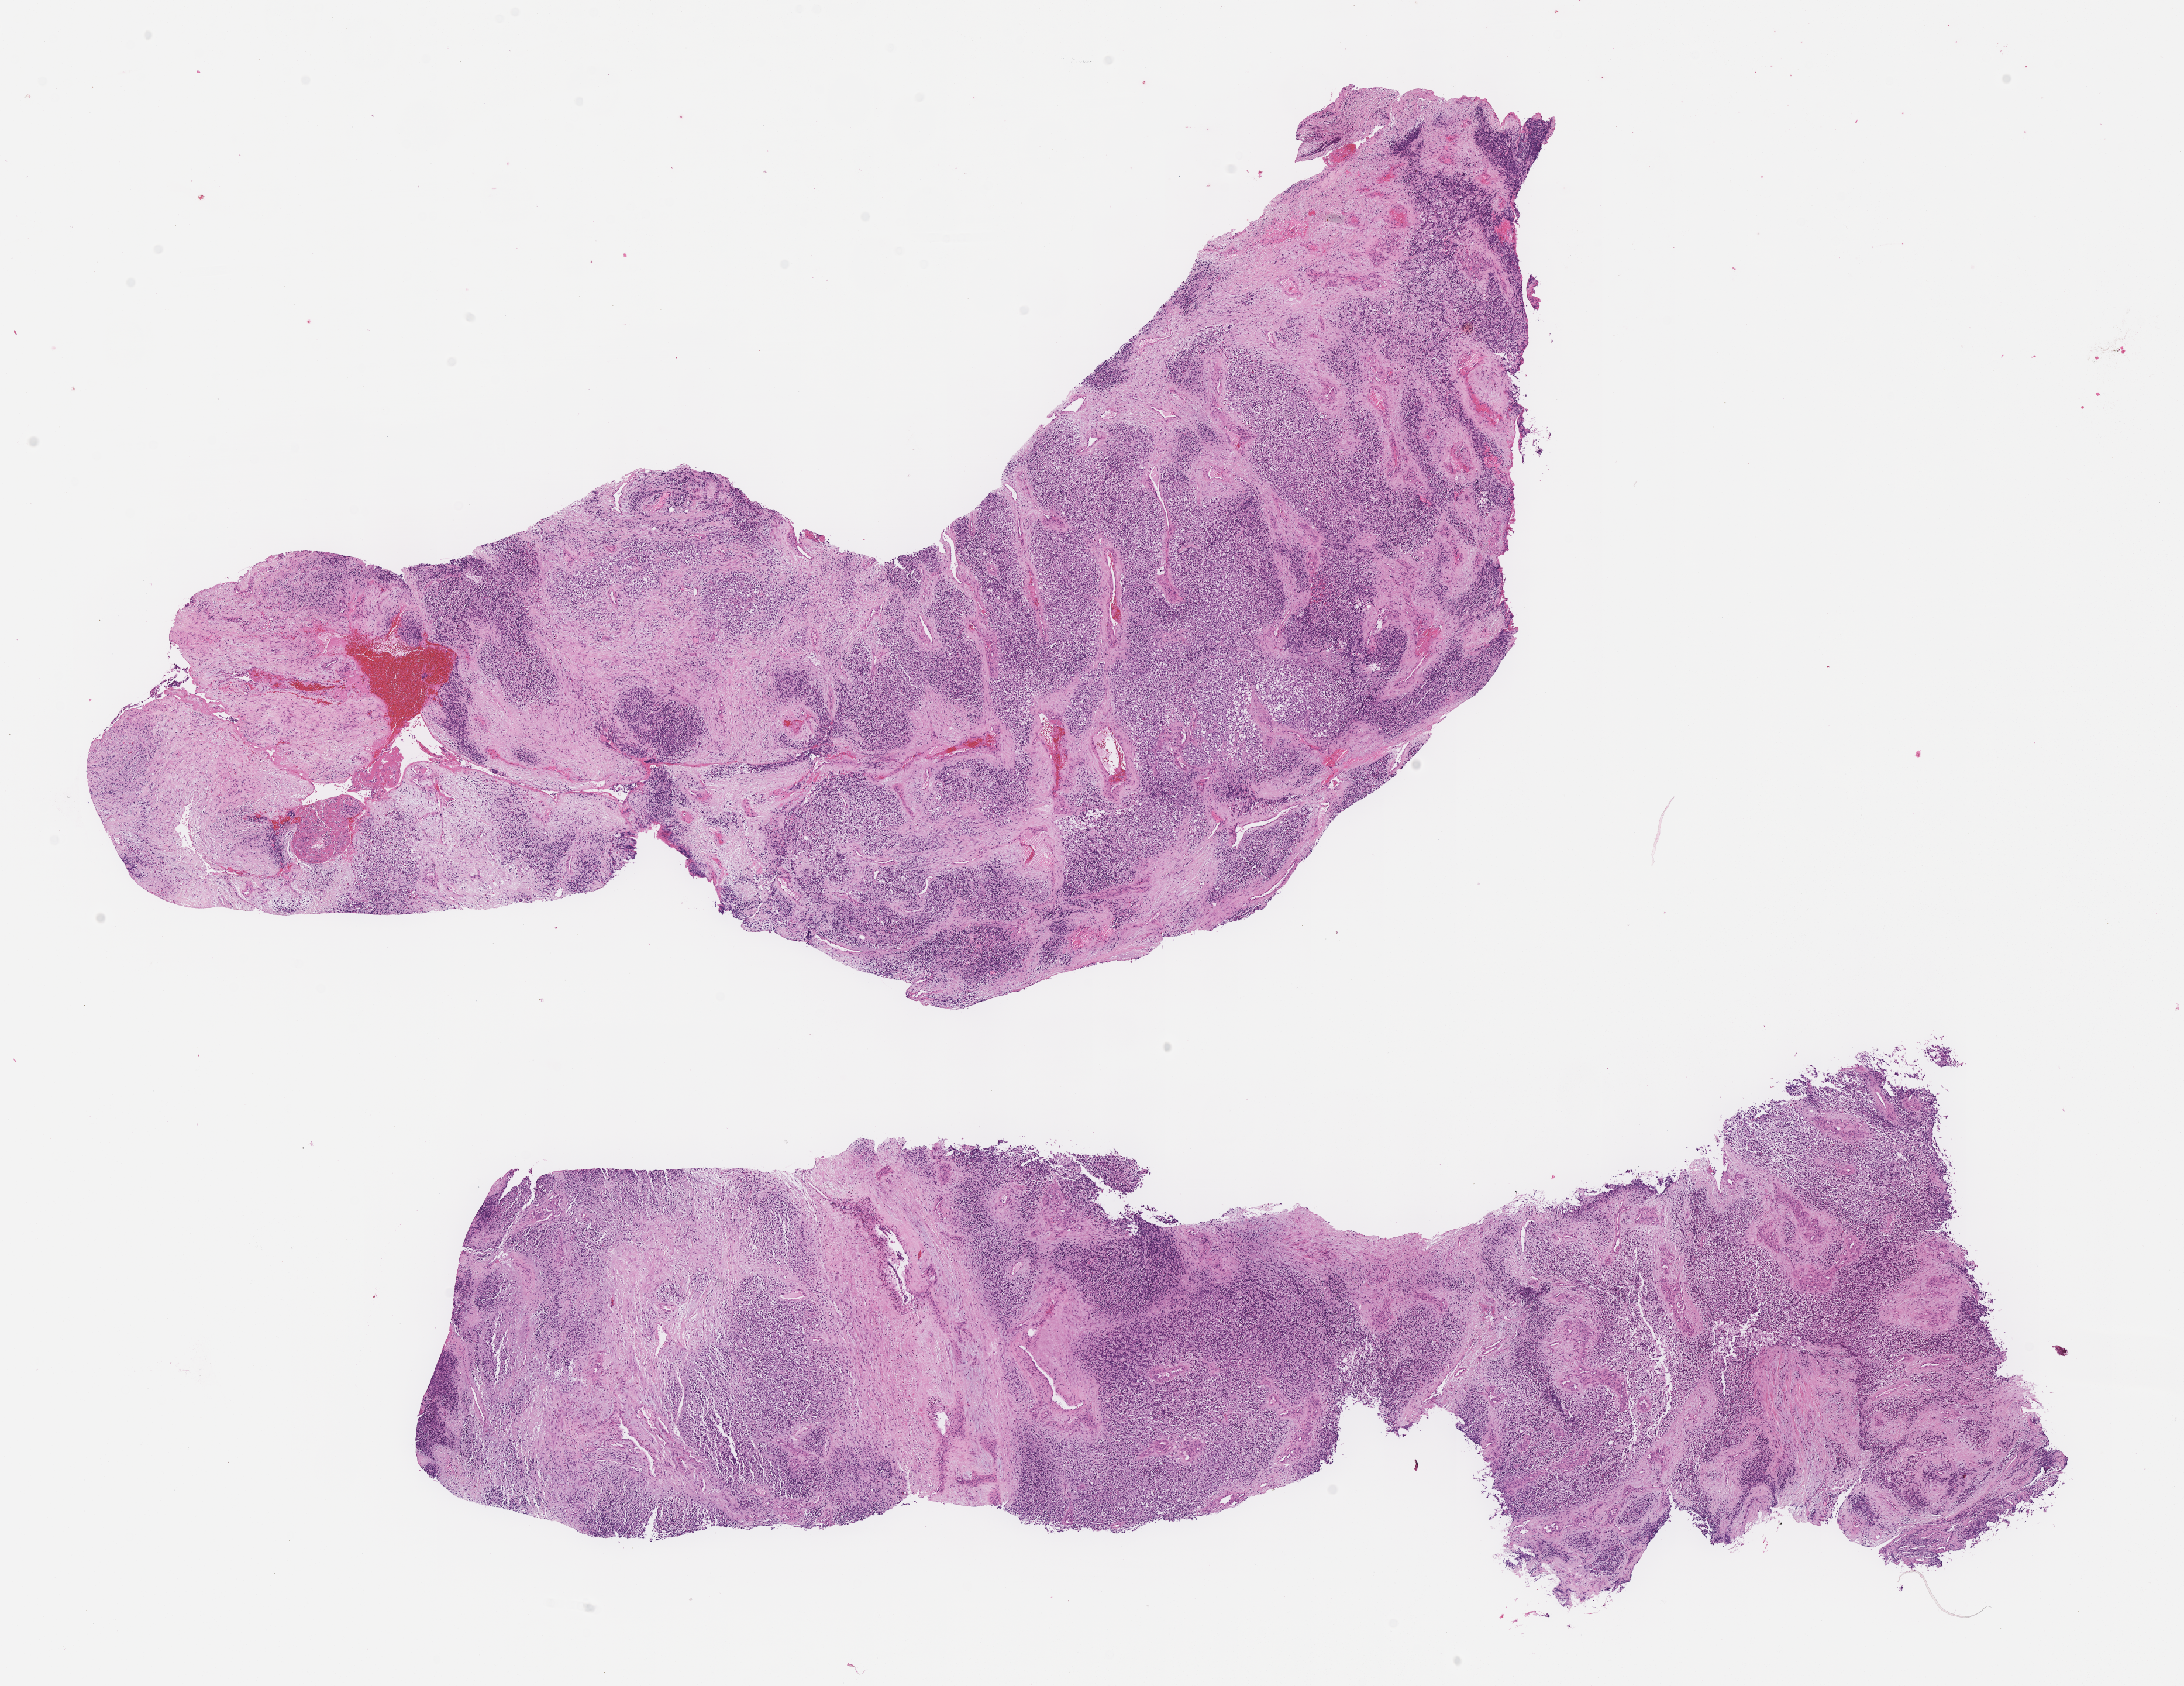
Whole-slide image, haematoxylin and eosin stain of tumor tissue — a low-resolution overview of the entire scanned area, about 15.1 x 11.7 mm. Formalin-fixed paraffin-embedded section. Sample anatomic site: pelvis. Patient: male, age 4.8 years at diagnosis.
- metastatic status at presentation (as recorded): non-metastatic (confirmed)
- diagnosis: rhabdomyosarcoma; histological classification: alveolar rhabdomyosarcoma
- stage (as recorded): 2